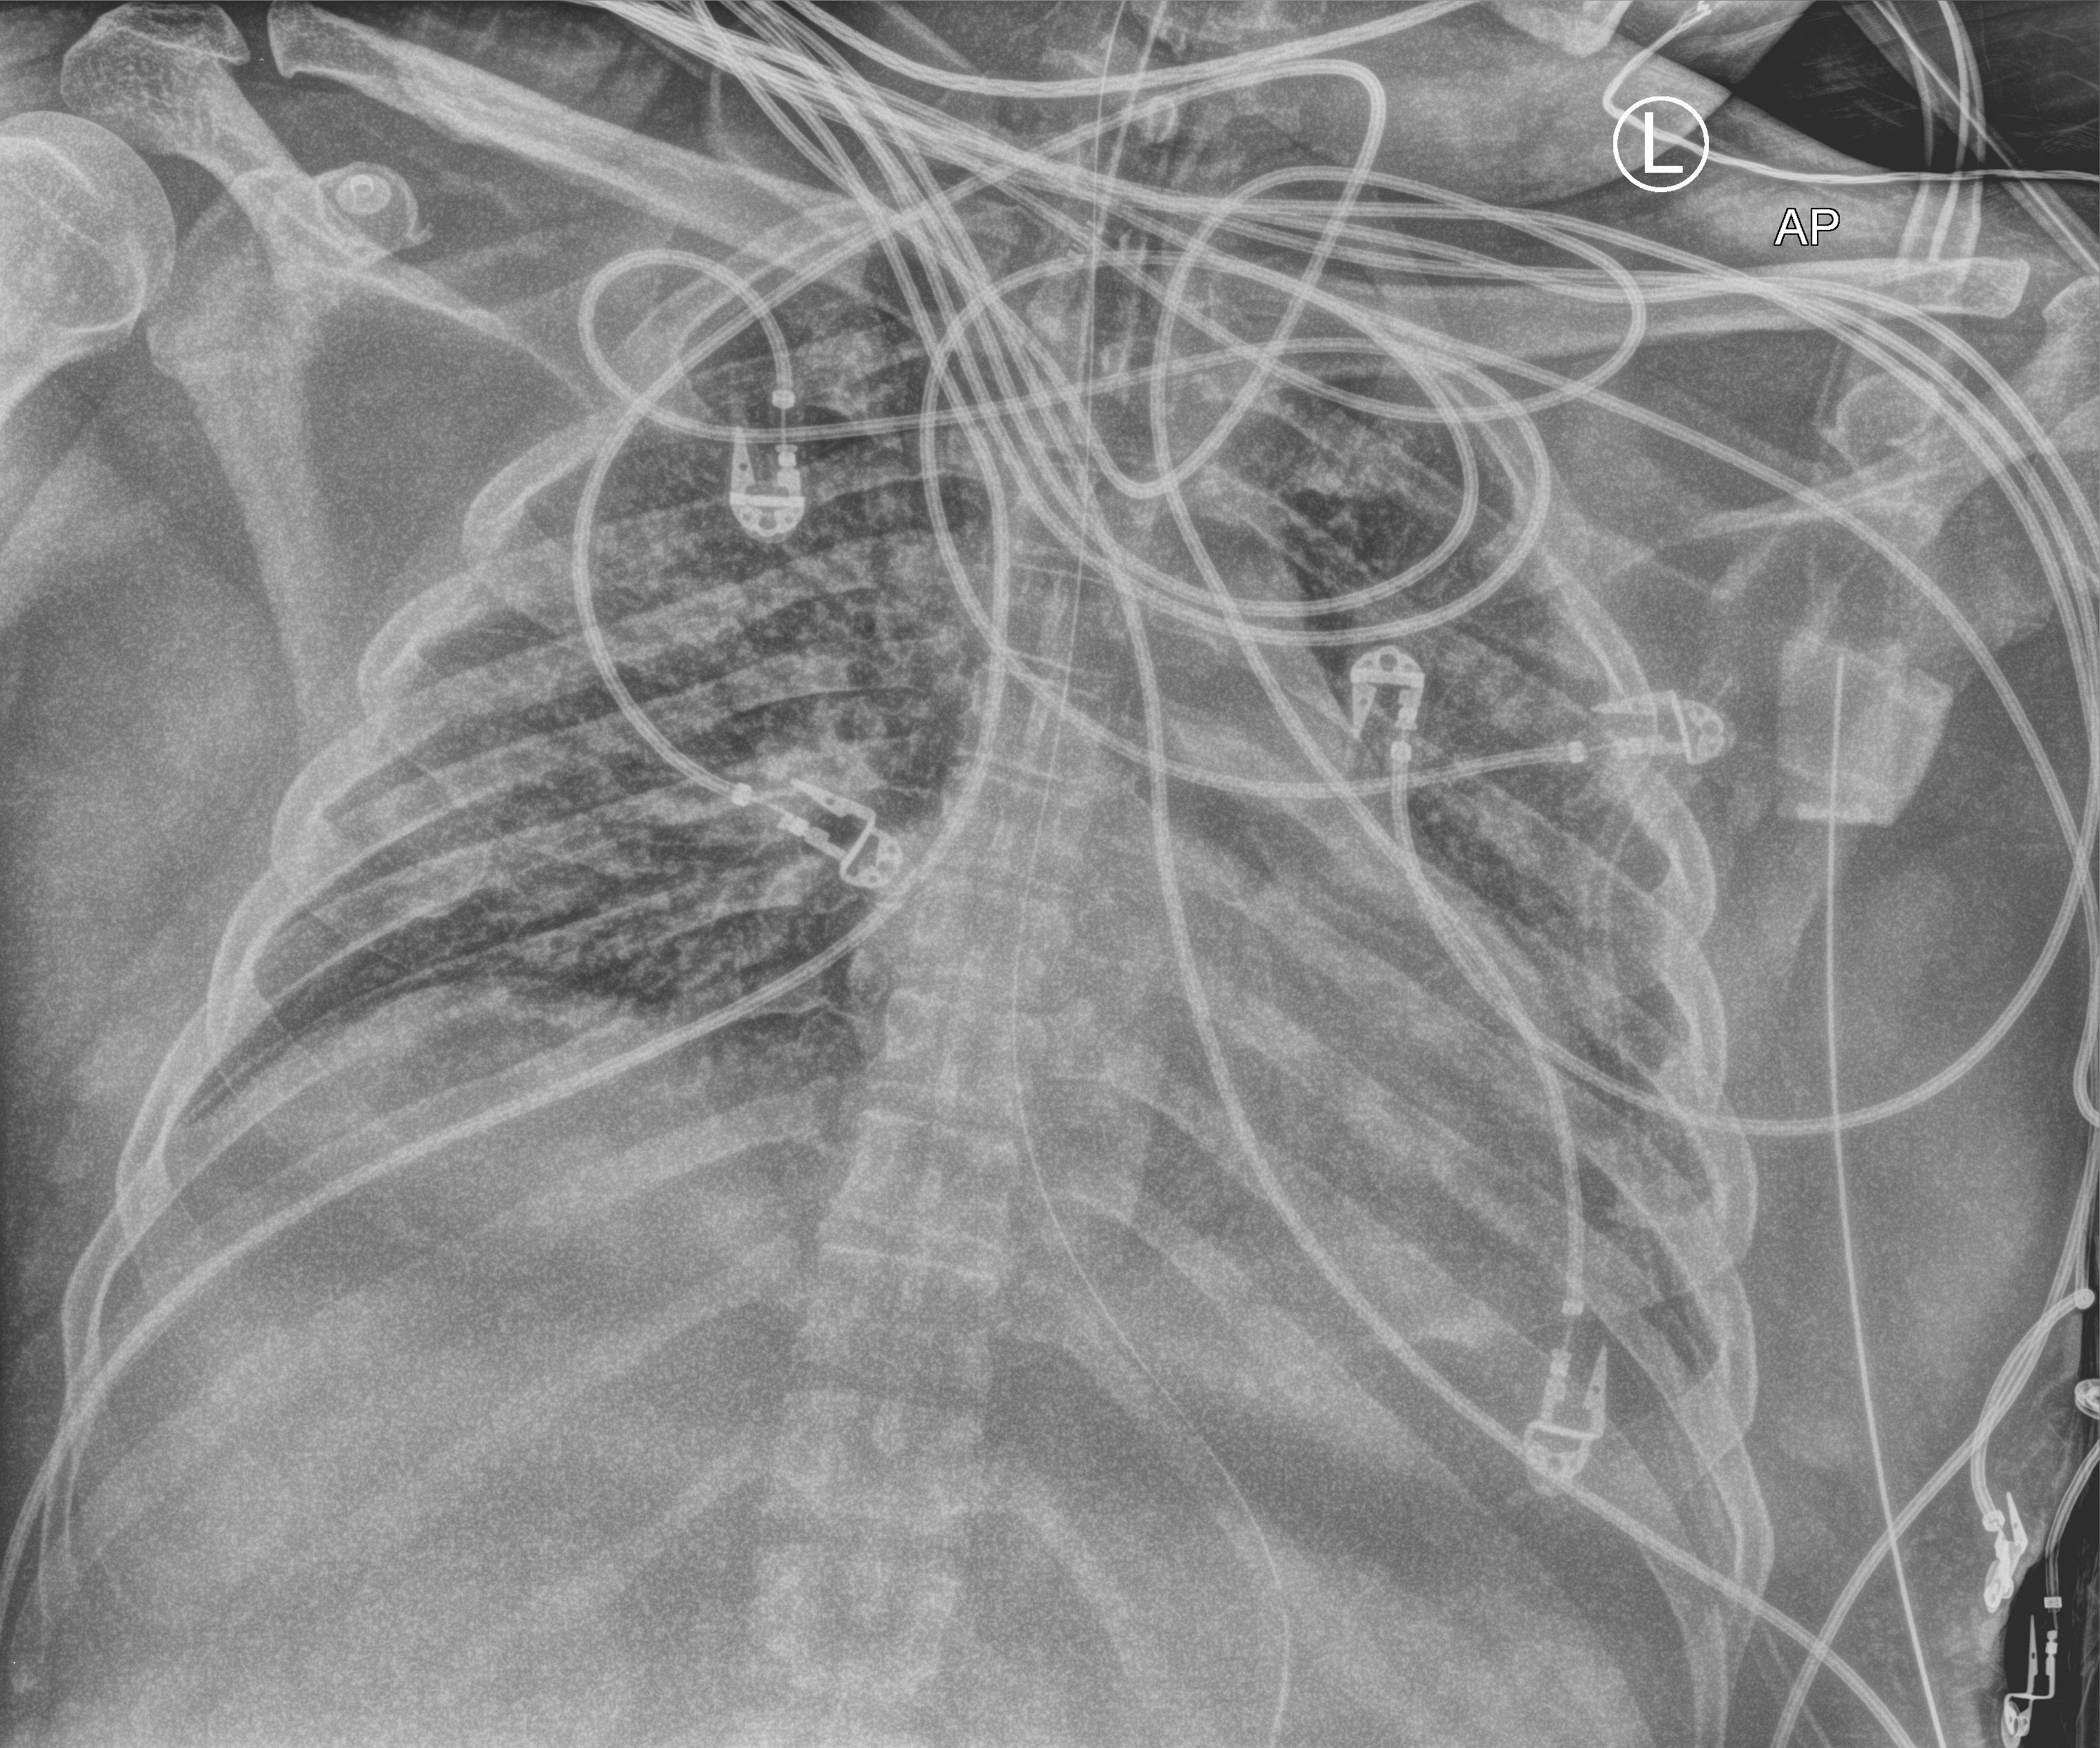
Chest X-ray (portable). Adult patient hospitalised with COVID-19, age 18–59 years.
From the hospital-stay record, not from the radiograph (when in the stay this image was taken is not recorded): hypertension (admission record): yes; admitted to intensive care during this hospital stay: yes.